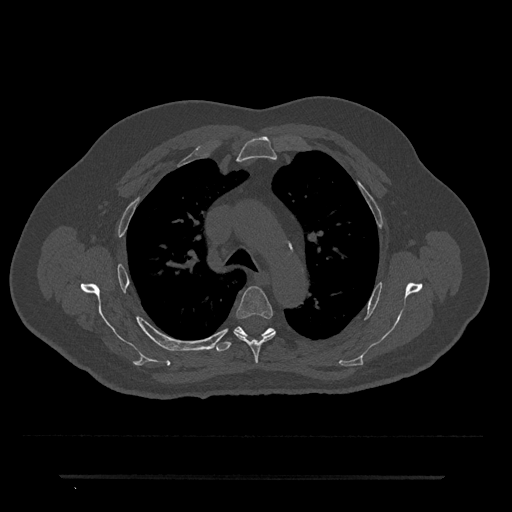
CT including the spine, one axial slice. Reconstruction kernel Br40s/3. 120 kVp. Bone window (W 1800 / L 400 HU). 512 × 512 image matrix, field of view 437 × 437 mm. Patient: male, 69 years. Case-level facts recorded for this patient, not image findings: primary cancer: prostate.
Structures marked on this image (semi-automatic segmentation, software-assisted and operator-edited):
- T4 vertebra: bounding box (x1, y1, x2, y2) in pixels: (234, 286, 276, 363)
- T5 vertebra: (214, 326, 275, 352)